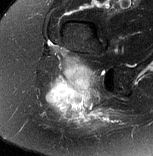
MRI of an extremity soft-tissue mass, one axial slice. Position 52 of 77 along the scan axis. T2-weighted fat-saturated. MR volume resampled by the dataset authors to the PET/CT grid (not the native acquisition matrix). 153 × 156 image matrix, field of view 149 × 152 mm. Female patient. From the clinical record (not read from this slice): histological type: synovial sarcoma; grade: intermediate; site of the primary tumour: right buttock.
Structures marked on this image (expert contour drawn on MRI and transferred to this co-registered scan by the dataset authors):
- gross tumour volume including surrounding oedema: bounding box <48,65,120,126> (left, top, right, bottom; pixels)
- gross tumour volume (mass): <48,65,95,100>